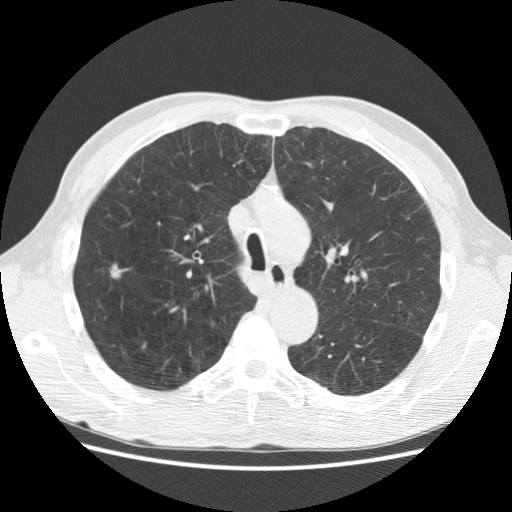
Low-dose screening chest CT, one axial slice; slice 205 of 282 in the series (ordered by position); reconstruction kernel STANDARD; lung window (W 1500 / L -600 HU); 2.5 mm slice thickness; 512 × 512 image matrix.
Outlined on this slice (expert manual segmentation):
- lesion 1 (tumor, upper lobe of right lung): box from (x=111, y=265) to (x=125, y=278) px